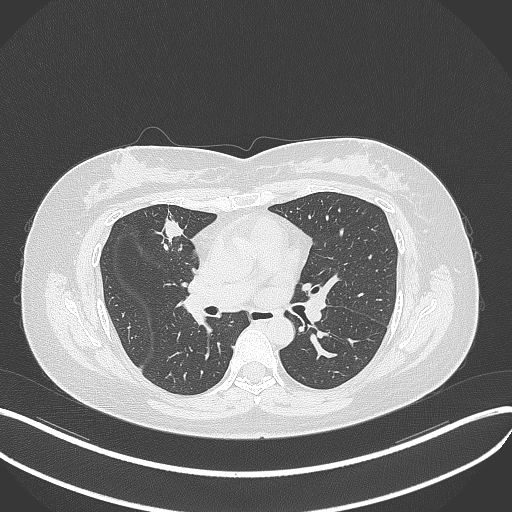
Chest CT, one axial slice; slice 173 of 273 in the series (ordered by position); reconstruction kernel B70f; 120 kVp; lung window (W 1500 / L -600 HU); 1 mm slice thickness; 512 × 512 image matrix, field of view 400 × 400 mm. Female patient, age 42 years. Case-level facts recorded for this patient, not image findings: clinical TNM (as recorded): T1b N0 M0.
Structures marked on this image (rectangle marked by the reading radiologist):
- lung tumour (recorded histology: adenocarcinoma): bounding box <152,212,187,243> (left, top, right, bottom; pixels)